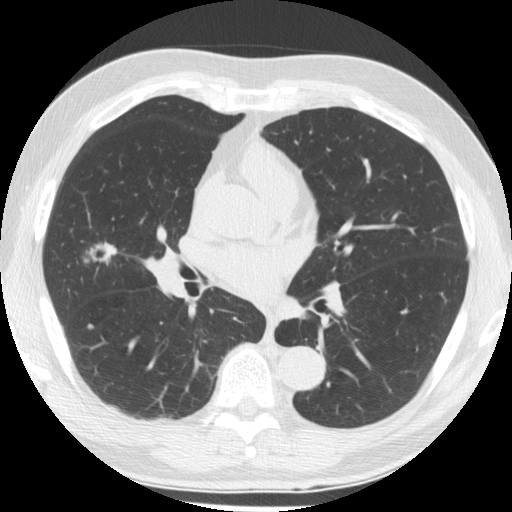
Axial slice from a low-dose chest CT screening exam, first (baseline) screen, lung window (W 1500 / L -600 HU), 2.5 mm slice thickness, standard (soft-tissue) reconstruction kernel (STANDARD). Male, age 64 years at enrolment.
Lesion marked by an expert reader, box from (x=60, y=221) to (x=128, y=285) px. The screening reader recorded 2 non-calcified nodules or masses ≥4 mm on this exam (right middle lobe, left lower lobe); which of them this box marks is not recorded. Official screen result: positive, change unspecified: nodule(s) >= 4 mm or enlarging nodule(s), mass(es), or other non-specific abnormalities suspicious for lung cancer. Participant outcome: lung cancer diagnosed 58 days after this screen — papillary adenocarcinoma, NOS, right middle lobe, well differentiated (G1), stage IA (AJCC 6th edition), 25 mm at pathology.